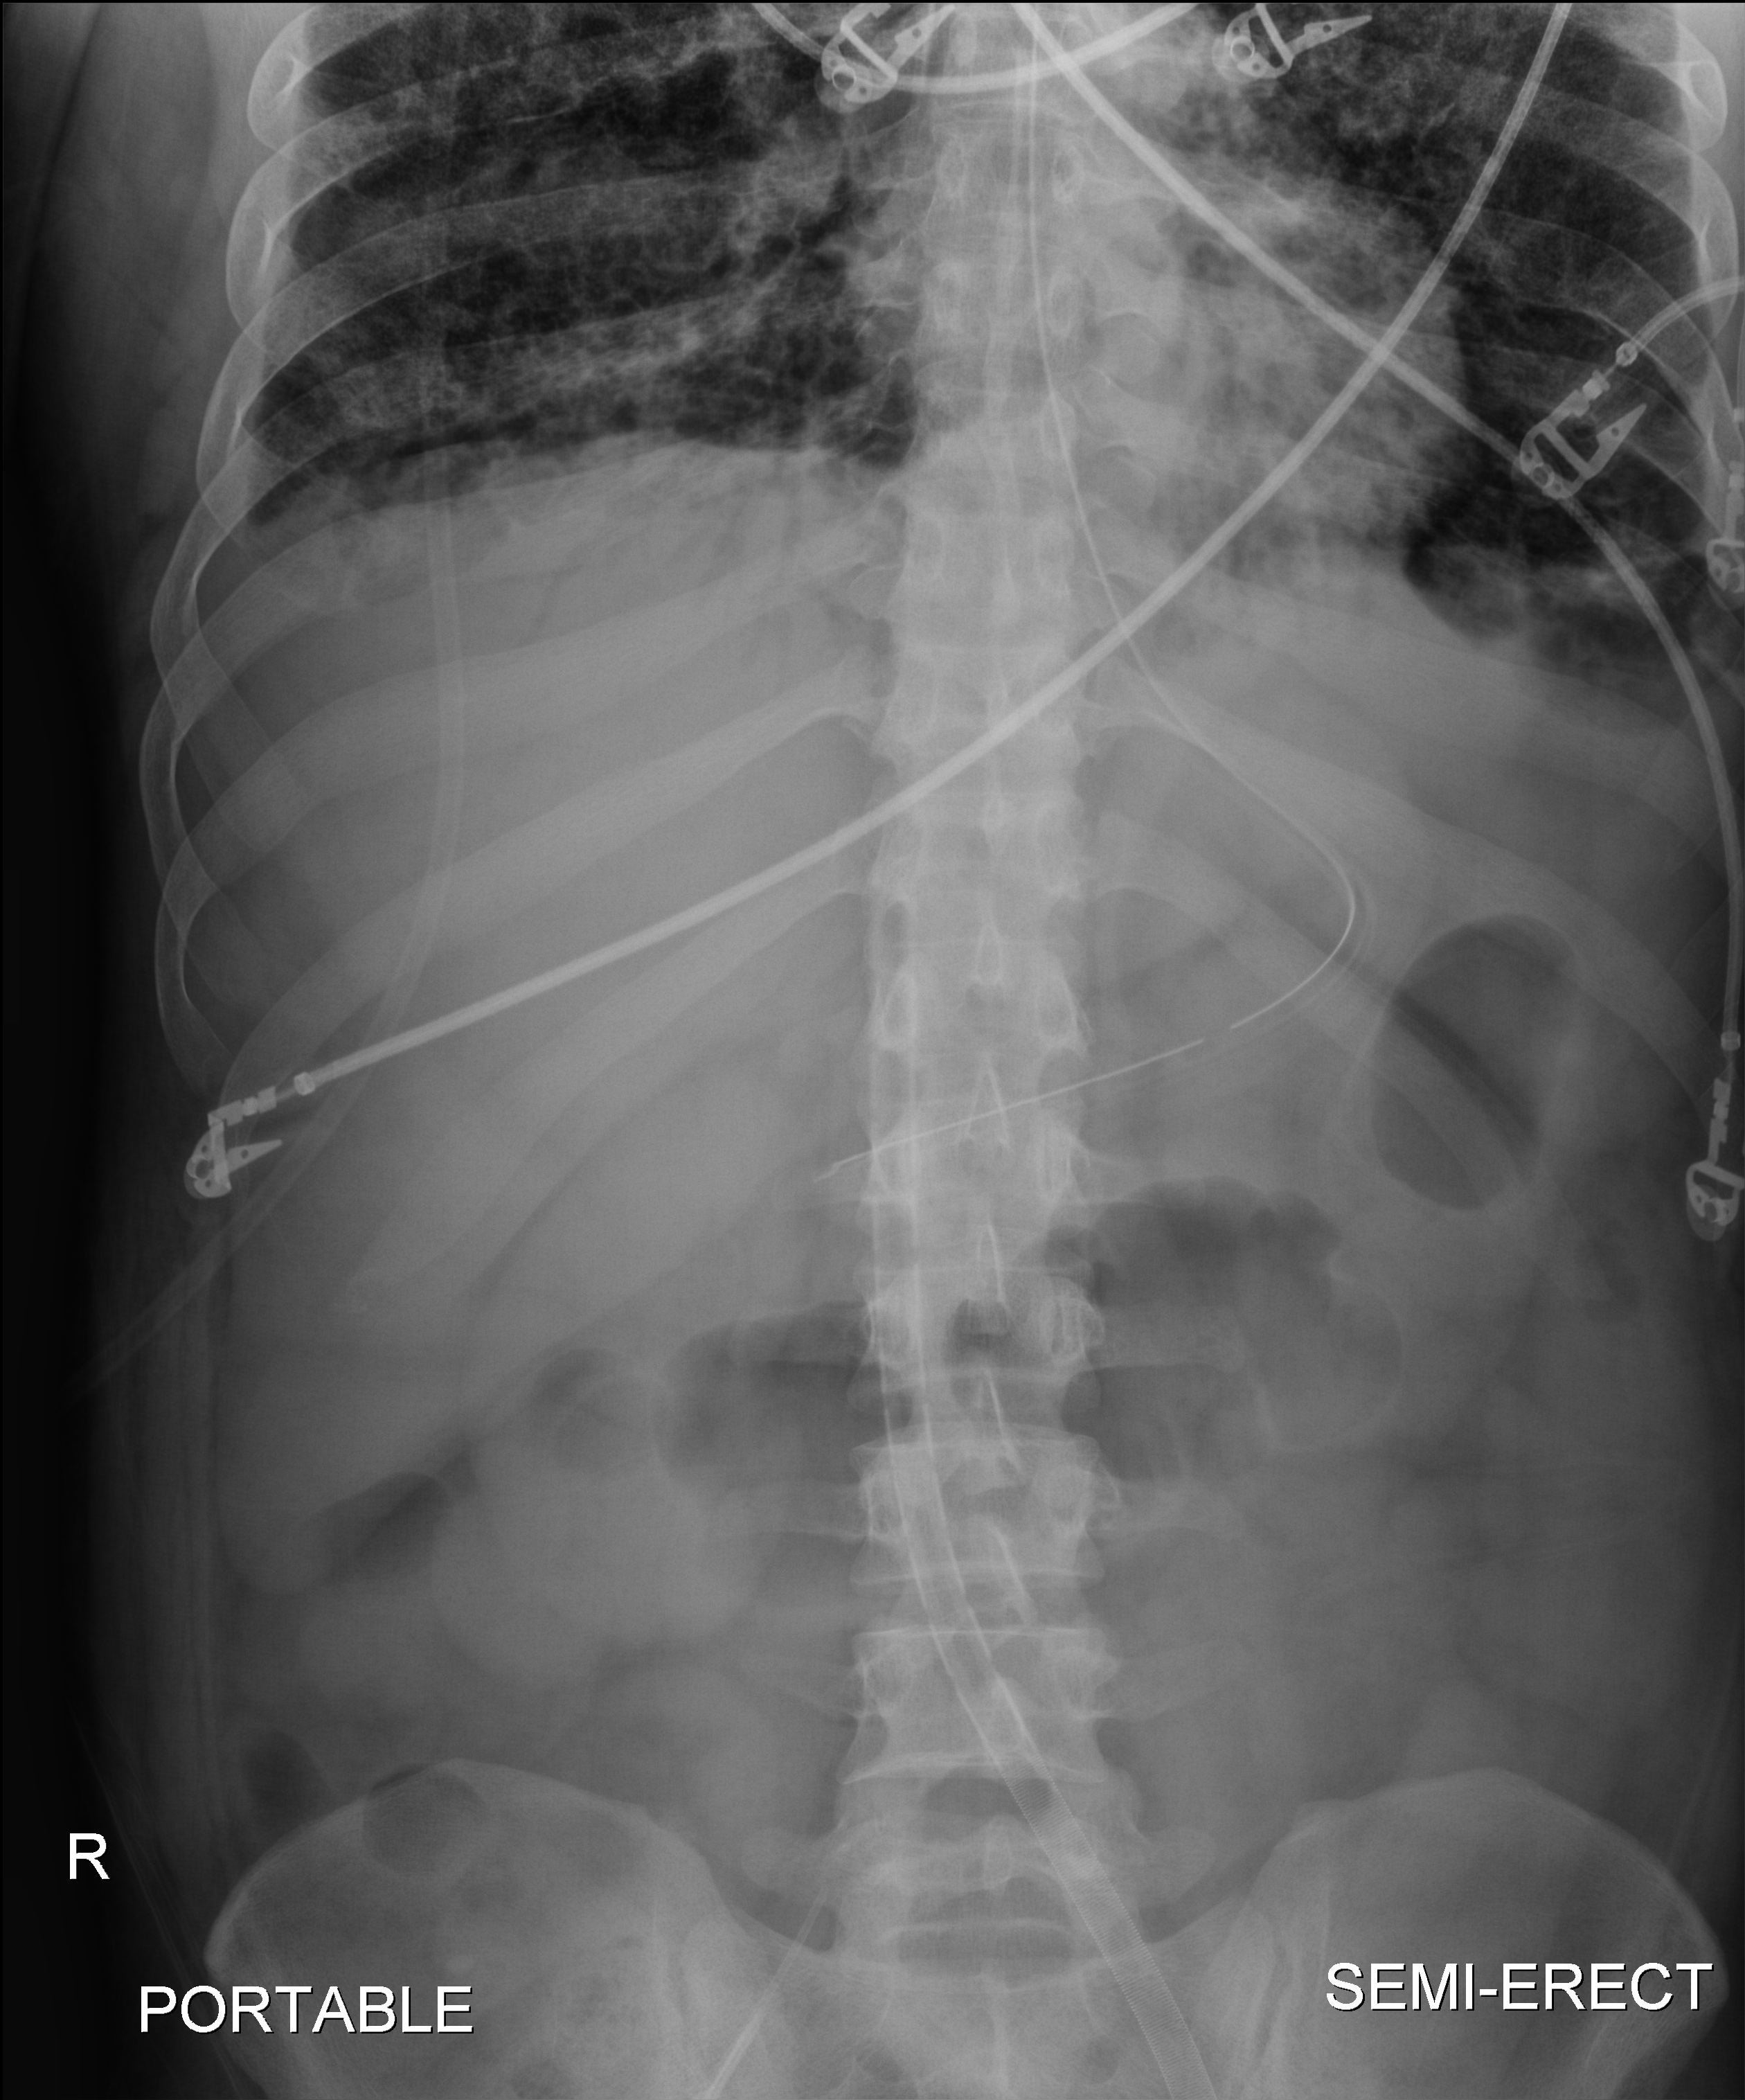
Bedside abdomen radiograph (digital radiography), anteroposterior (AP) projection. Patient hospitalised with COVID-19, aged 18–59 years.
Hospital-stay facts (about this admission, not read from this image; timing relative to this image not recorded): admitted to intensive care during this hospital stay: yes; mechanically ventilated during this hospital stay: yes; hypertension (admission record): no.